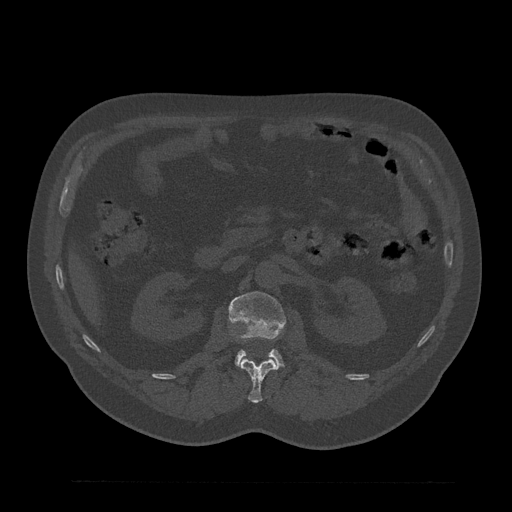
CT including the spine, one axial slice; position 133 of 797 along the scan axis; 120 kVp; bone window (W 1800 / L 400 HU); 0.5 mm slice thickness; 512 × 512 image matrix, field of view 430 × 430 mm. Male patient, age 61 years. Case-level facts recorded for this patient, not image findings: primary cancer: prostate.
Outlined on this slice (semi-automatically segmented with operator editing):
- L1 vertebra: box from (x=240, y=359) to (x=278, y=403) px
- L2 vertebra: (x=229, y=292)–(x=285, y=367)